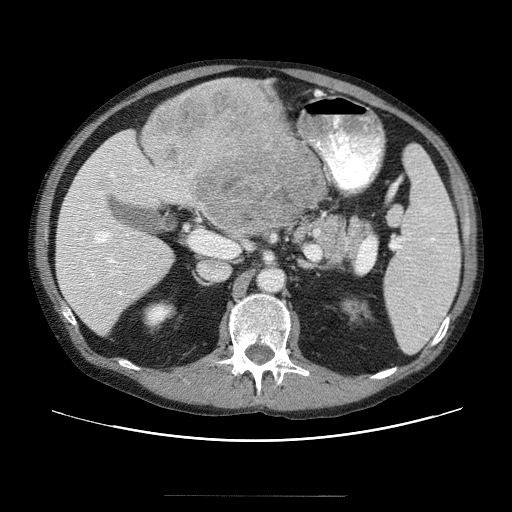
Contrast-enhanced abdominal CT (liver protocol), one axial slice. Position 19 of 69 along the scan axis. Reconstruction kernel STANDARD. 120 kVp. Soft-tissue window (W 400 / L 40 HU). 2.5 mm slice thickness. 512 × 512 image matrix. From the clinical record (not read from this slice): diagnosis: hepatocellular carcinoma (patient treated with transarterial chemoembolisation; whether this scan precedes or follows treatment is not stated here); TNM stage (as recorded): Stage-IVB.
Annotated regions visible in this slice (semi-automatic segmentation, software-assisted and operator-edited):
- liver parenchyma outside the tumour (the mass and vessels are separate outlines, so this box may not span the whole liver): box from (x=54, y=110) to (x=203, y=330) px
- mass: (x=143, y=80)–(x=329, y=236)
- liver vessels: (x=62, y=162)–(x=145, y=314)